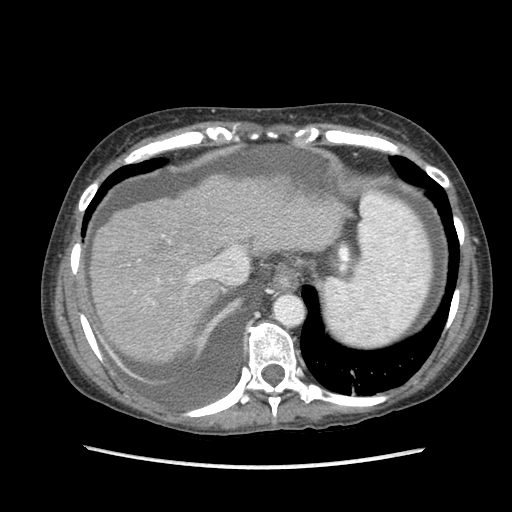
Contrast-enhanced abdominal CT (liver protocol), one axial slice. Slice 74 of 87 in the series (ordered by position). Reconstruction kernel STANDARD. Soft-tissue window (W 400 / L 40 HU). 2.5 mm slice thickness. 512 × 512 image matrix, field of view 340 × 340 mm. Case-level facts recorded for this patient, not image findings: diagnosis: hepatocellular carcinoma (patient treated with transarterial chemoembolisation; whether this scan precedes or follows treatment is not stated here); TNM stage (as recorded): Stage-IIIB; Child-Pugh class: A; tumour nodularity: uninodular.
Outlined on this slice (semi-automatically segmented with operator editing):
- liver parenchyma outside the tumour (the mass and vessels are separate outlines, so this box may not span the whole liver): box from (x=90, y=174) to (x=346, y=360) px
- liver vessels: (x=134, y=248)–(x=247, y=293)